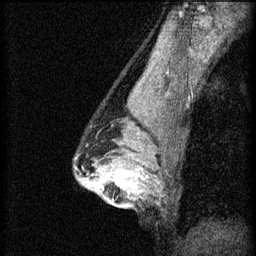
Breast MRI (dynamic contrast-enhanced), one sagittal slice. Position 42 of 60 along the scan axis. 3 images stored at this slice position (order not interpretable as contrast timing). 1.5 T. TE 4.2 ms, TR 8.2 ms. 256 × 256 image matrix, field of view 180 × 180 mm. Patient: female, 44 years.
Annotated regions visible in this slice (semi-automatically segmented with operator editing):
- analysis volume of interest (the breast-tissue region the enhancement analysis was run in; not a lesion): bounding box [x1, y1, x2, y2] px = [94, 162, 143, 205]
- tumour enhancement mask (voxels above the 70 % enhancement threshold inside the analysis volume of interest): [100, 168, 143, 201]